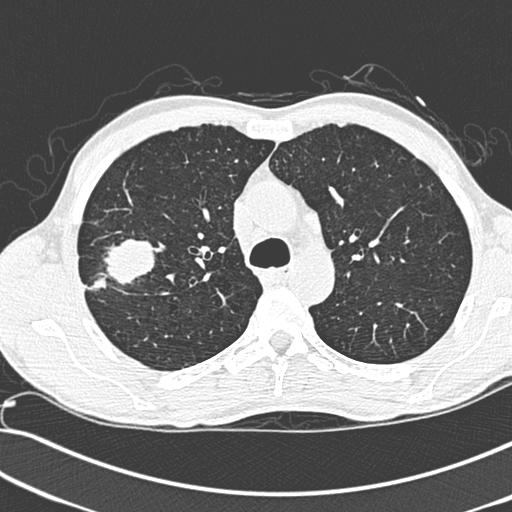
Low-dose screening chest CT, one axial slice; slice 208 of 281 in the series (ordered by position); 120 kVp; lung window (W 1500 / L -600 HU); 1.3 mm slice thickness; 512 × 512 image matrix, field of view 341 × 341 mm.
Annotated regions visible in this slice (expert manual segmentation):
- lesion 1 (tumor, upper lobe of right lung): bounding box (x1, y1, x2, y2) in pixels: (87, 239, 158, 295)